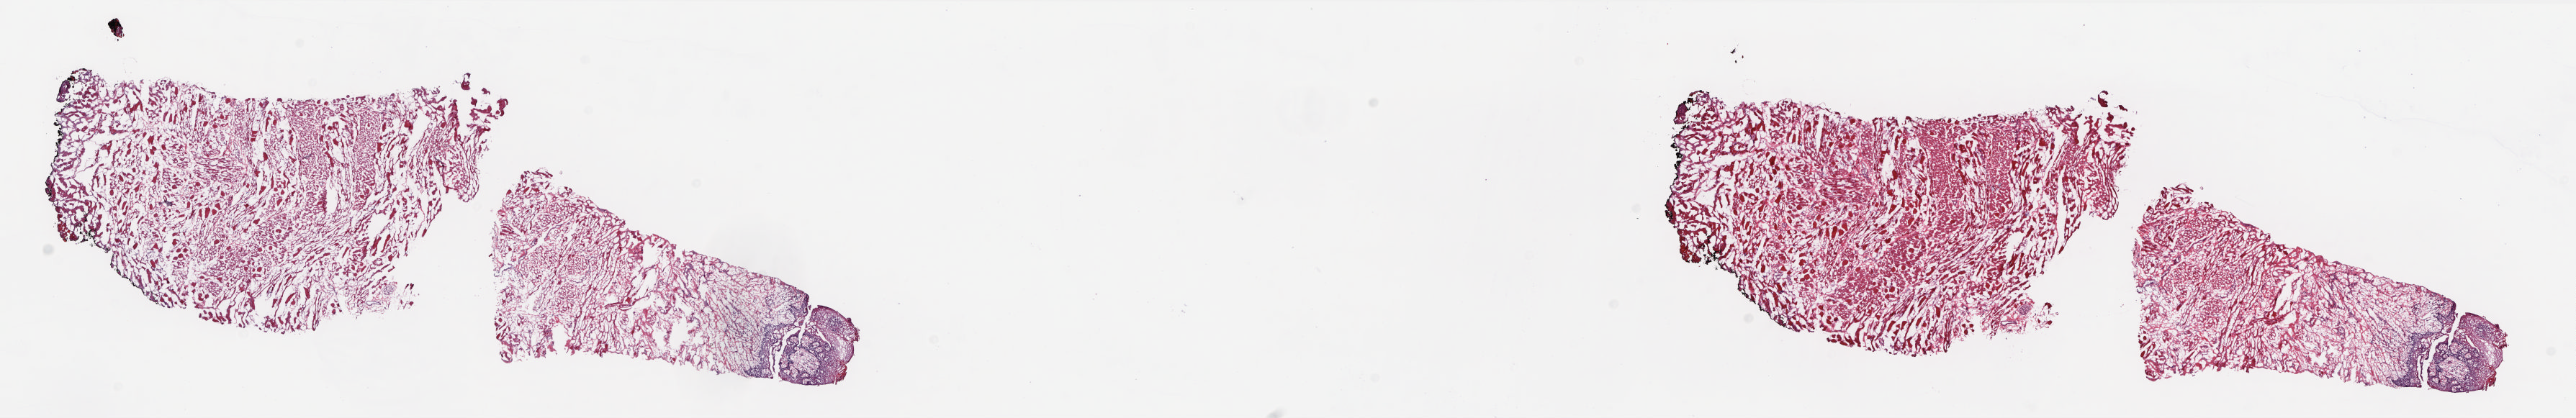
Hematoxylin and eosin (H&E) stained whole-slide image — a low-resolution overview of the entire scanned area, about 28.9 x 4.7 mm (slide scanned at 20x). Frozen section from the top of the tissue portion. Solid tissue normal (non-tumour tissue) sample from the head and neck. Patient: female, age at initial diagnosis 35 years. Pathologist review of this section (percent, as recorded): tumour cells 0%, tumour nuclei 0%.
This section: solid tissue normal (non-tumour) sample from the same patient. Patient diagnosis: Squamous cell carcinoma, keratinizing, NOS (tongue, NOS).